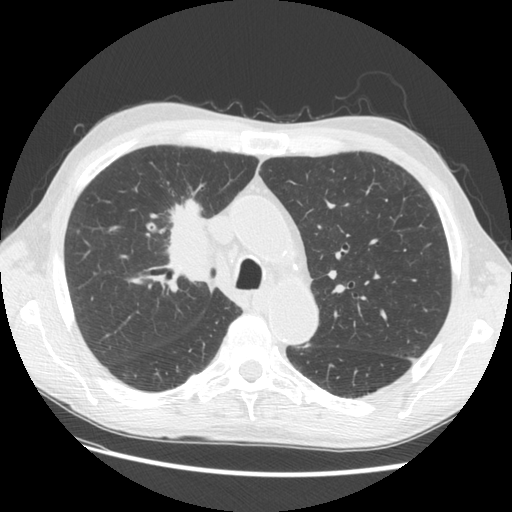
Low-dose screening chest CT, one axial slice; position 93 of 133 along the scan axis; reconstruction kernel STANDARD; 120 kVp; lung window (W 1500 / L -600 HU); 2.5 mm slice thickness; 512 × 512 image matrix.
Annotated regions visible in this slice (expert manual segmentation):
- lesion 1 (tumor, hilum of right lung): bounding box (x1, y1, x2, y2) in pixels: (167, 198, 212, 279)